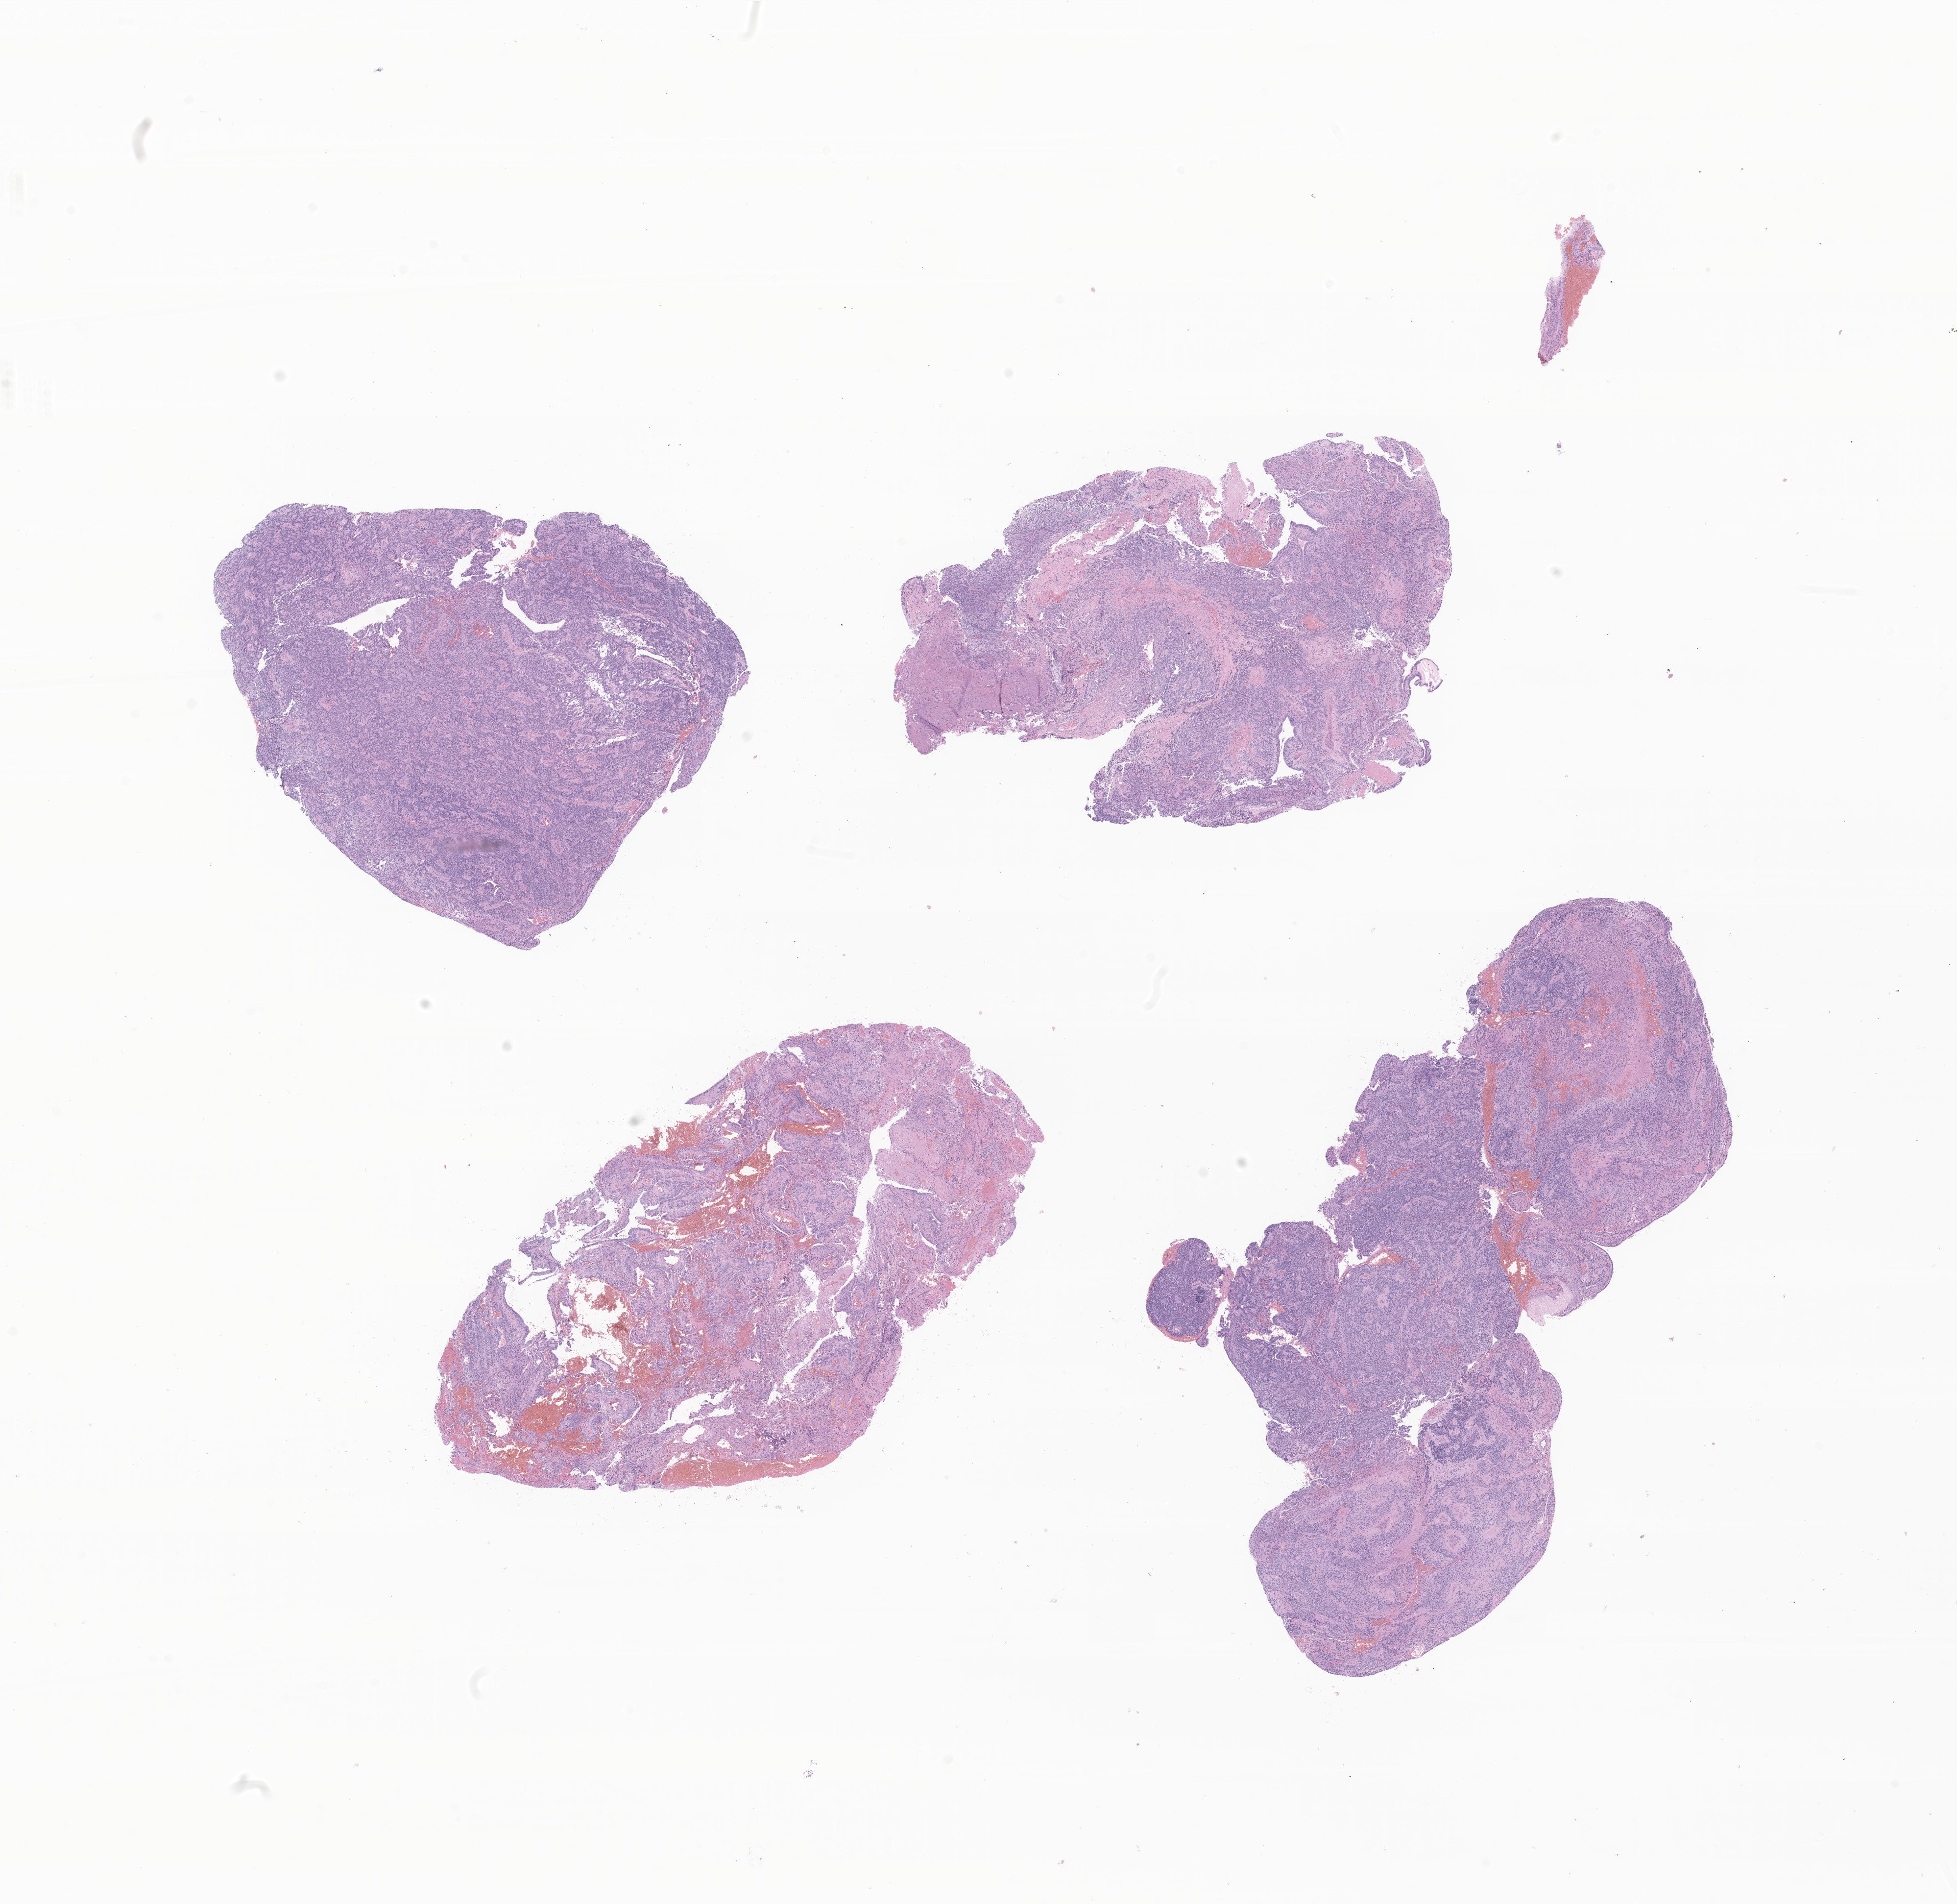
Hematoxylin and eosin (H&E) whole-slide image of tumor tissue from the brain, low-resolution overview of the scanned area, about 16.8 x 16.4 mm; formalin-fixed paraffin-embedded section. Female patient, age 152 months (12 years 8 months).
Diagnosis: Ependymoma, NOS.